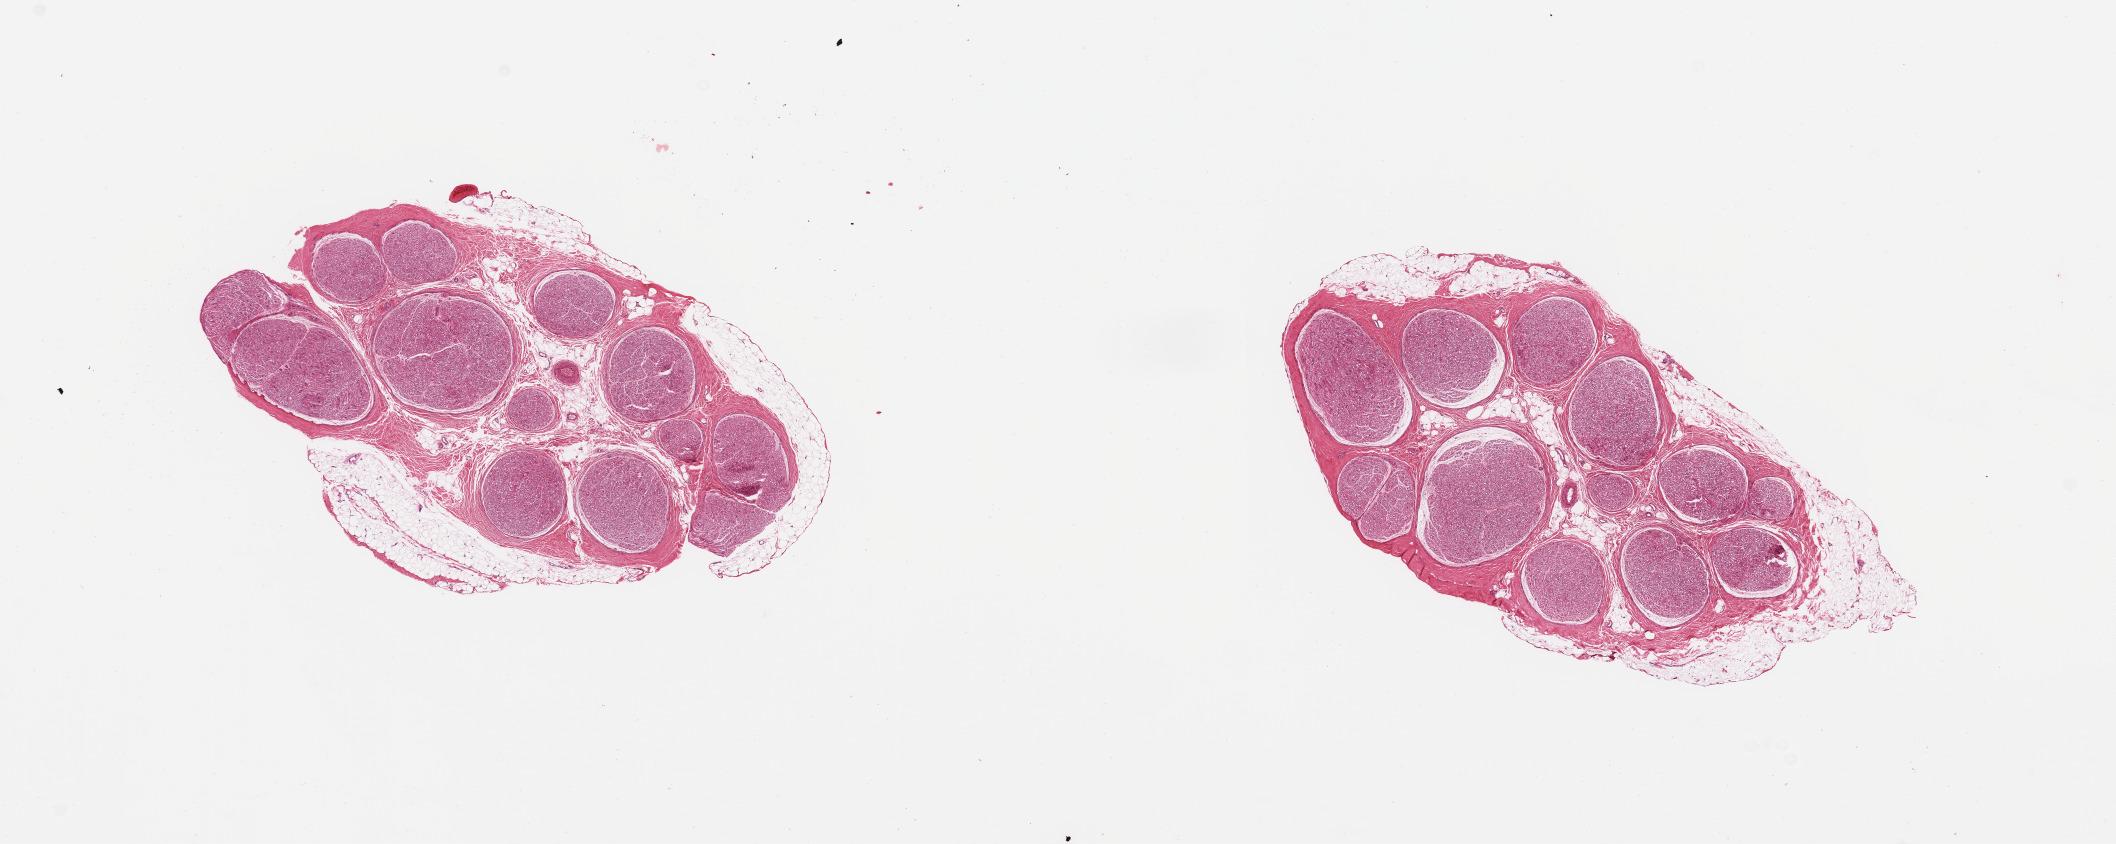
Whole-slide image, H&E stain — a low-resolution overview of the entire scanned area, about 16.7 x 6.7 mm; PAXgene-fixed, paraffin-embedded tissue; sampled site (target tissue): tibial nerve; donor tissue sample. Male donor.
- pathologist's review note for this sample: 2 pieces; includes partial rim of fat (~10%)